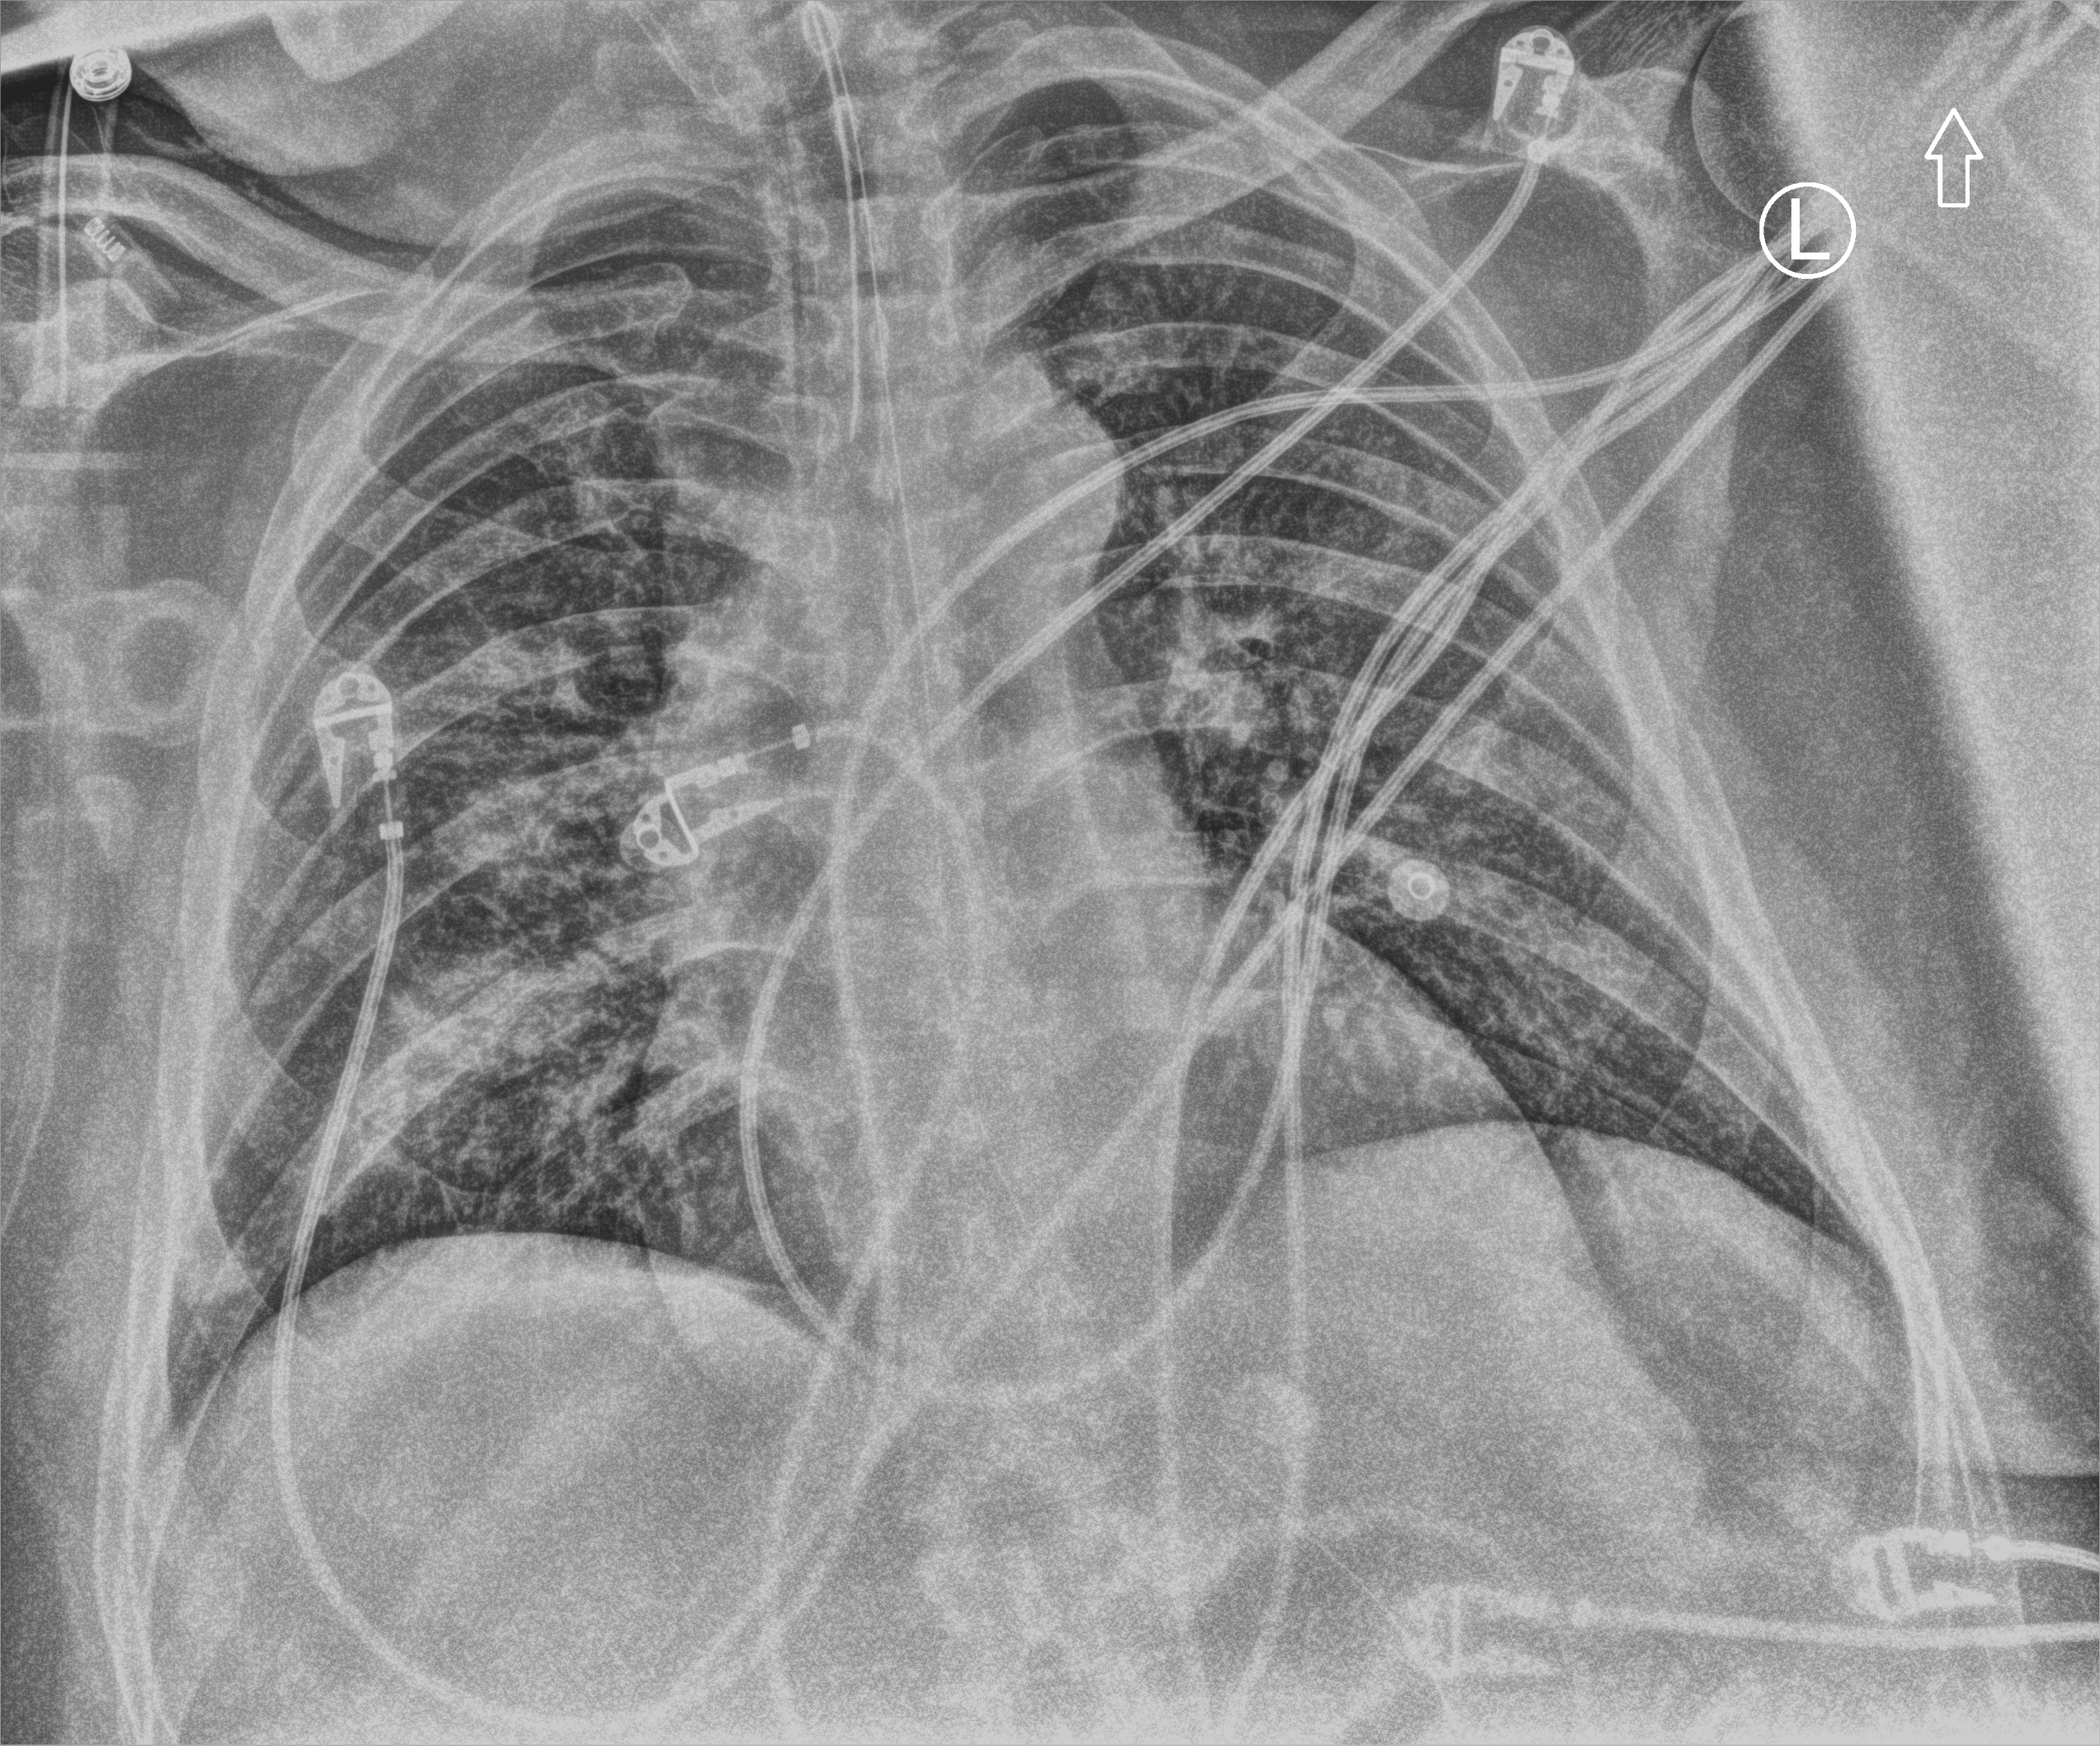
Bedside chest radiograph (computed radiography). Patient hospitalised with COVID-19; male, aged 60–74 years.
Hospital-stay facts (about this admission, not read from this image; timing relative to this image not recorded): admitted to intensive care during this hospital stay: yes; smoking status (admission record): former; mechanically ventilated during this hospital stay: yes.